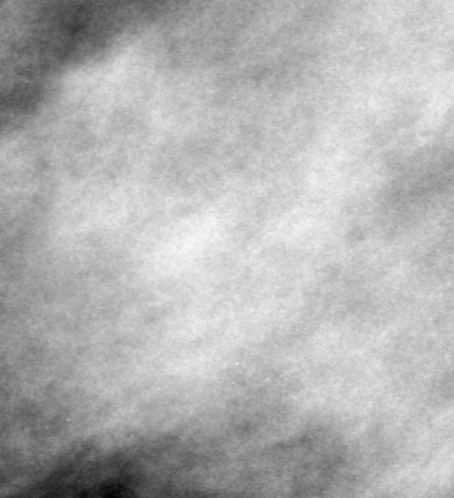
Region of interest cut from a scanned film mammogram (one marked finding); right breast; MLO view.
Mass, shape oval, margins obscured; BI-RADS assessment category 0; pathology result (as recorded, not read from the image): benign.